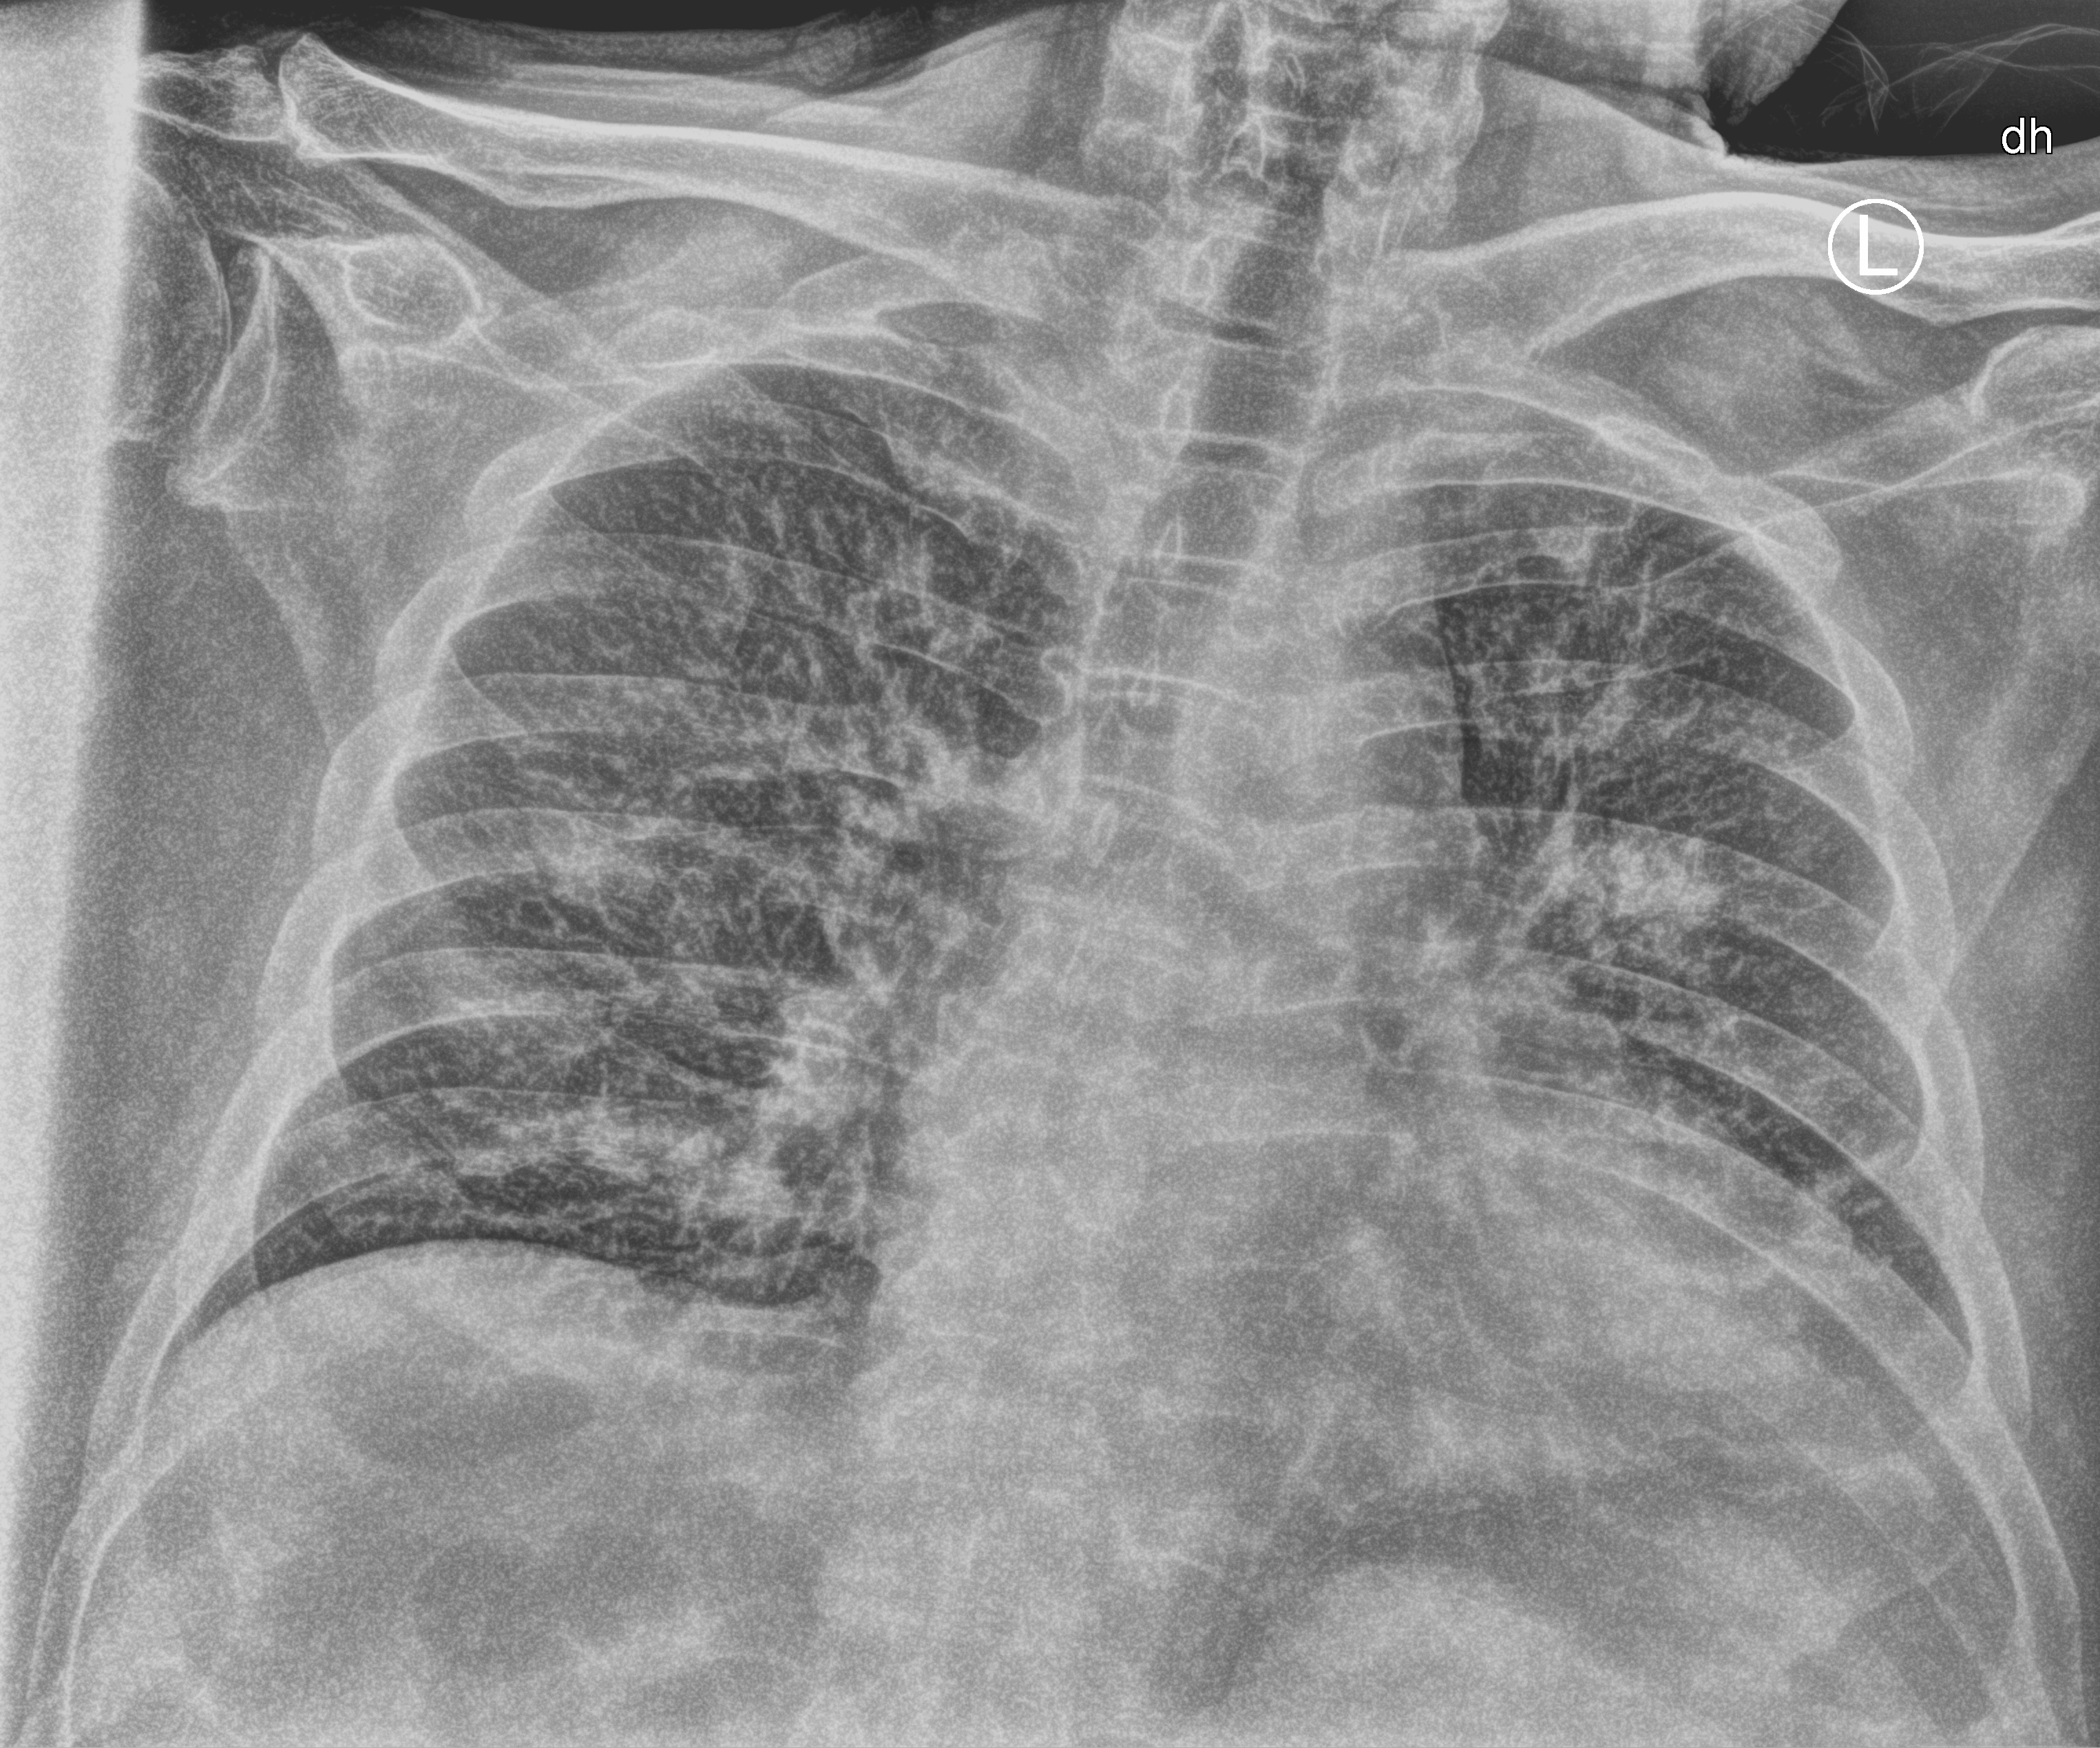
Chest X-ray (portable), anteroposterior (AP) projection. Patient hospitalised with COVID-19; male, aged 75–90 years.
Hospital-stay facts (about this admission, not read from this image; timing relative to this image not recorded):
- length of hospital stay: 1 day
- mechanically ventilated during this hospital stay: no